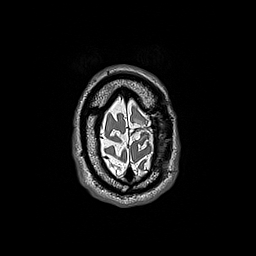
Brain MRI from a brain-tumour surgery series, one axial slice; position 34 of 192 along the scan axis; 1 mm slice thickness; 256 × 256 image matrix, field of view 250 × 250 mm. From the clinical record (not read from this slice): histopathology: Oligodendroglioma; WHO grade: 3; IDH mutation: yes; tumour location: Left Frontal.
Annotated regions visible in this slice (outlined manually by an expert reader):
- tumour: box from (x=136, y=120) to (x=144, y=126) px